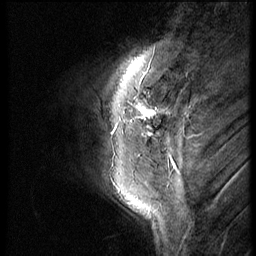
Breast MRI (dynamic contrast-enhanced), one sagittal slice; 3 images stored at this slice position (order not interpretable as contrast timing); 1.5 T; TE 4.2 ms, TR 9 ms; 2.5 mm slice thickness; 256 × 256 image matrix, field of view 180 × 180 mm. Patient: female, 46 years. From the clinical record (not read from this slice): setting: breast cancer imaged before/during neoadjuvant chemotherapy; receptor status: HER2-positive.
Outlined on this slice (semi-automatically segmented with operator editing):
- analysis volume of interest (the breast-tissue region the enhancement analysis was run in; not a lesion): bounding box <80,86,164,161> (left, top, right, bottom; pixels)
- tumour enhancement mask (voxels above the 140 % enhancement threshold inside the analysis volume of interest): <141,106,153,135>